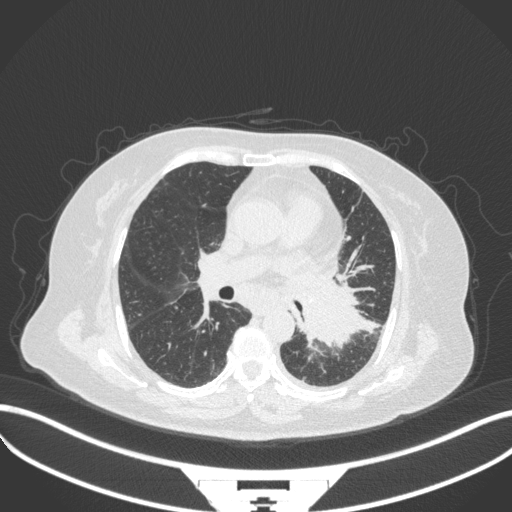
Chest CT, one axial slice. Slice 189 of 328 in the series (ordered by position). Reconstruction kernel B31f. Lung window (W 1500 / L -600 HU). 1 mm slice thickness. 512 × 512 image matrix. Female patient, age 69 years. Case-level facts recorded for this patient, not image findings: clinical TNM (as recorded): T2b N3 M1.
Structures marked on this image (bounding box drawn by a radiologist):
- lung tumour (recorded histology: adenocarcinoma): box from (x=292, y=274) to (x=368, y=356) px